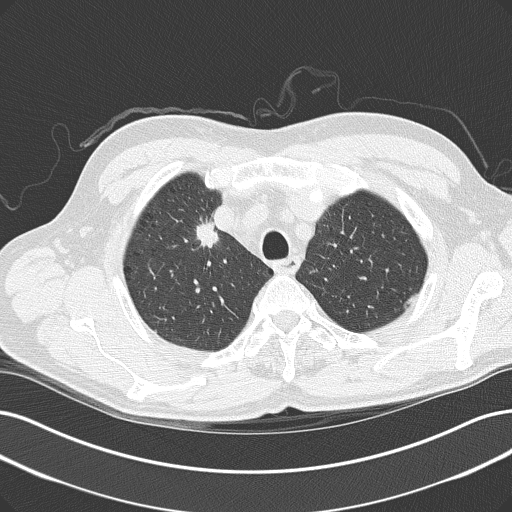
Low-dose screening chest CT, axial slice; first (baseline) screen; lung window (W 1500 / L -600 HU); 2 mm slice thickness; lung (sharp) reconstruction kernel (B50f); slice 31 of 152 in the series. Male participant, aged 61 years at enrolment. Current smoker at enrolment.
Expert-annotated lung lesion, bounding box (x1, y1, x2, y2) in pixels: (189, 220, 245, 267). The screening reader recorded 2 non-calcified nodules or masses ≥4 mm on this exam (right upper lobe, right upper lobe); which of them this box marks is not recorded. Later outcome: lung cancer diagnosed 54 days after this screen — adenocarcinoma, NOS, right upper lobe, poorly differentiated (G3), stage IIIB (AJCC 6th edition).